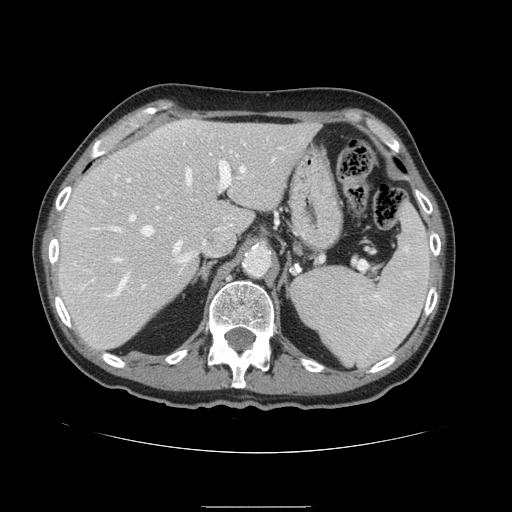
Contrast-enhanced abdominal CT, one axial slice; slice 105 of 168 in the series (ordered by position); 120 kVp; intravenous contrast given; soft-tissue window (W 400 / L 40 HU); 512 × 512 image matrix, field of view 386 × 386 mm. Male patient, age 74 years. From the clinical record (not read from this slice): diagnosis: colorectal cancer liver metastases, imaged before liver resection; multiple liver metastases: no; largest metastasis: 14.5 cm; disease in both lobes: yes.
Outlined on this slice (expert manual segmentation):
- hepatic veins: bounding box <114,167,245,291> (left, top, right, bottom; pixels)
- liver: <57,119,320,350>
- planned liver remnant (the part of the liver to remain after resection): <57,120,320,350>
- portal vein (with intrahepatic branches): <97,161,231,251>